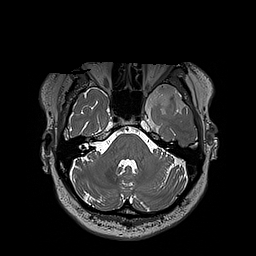
Brain MRI from a brain-tumour surgery series, one axial slice. Slice 147 of 192 in the series (ordered by position). 1 mm slice thickness. 256 × 256 image matrix, field of view 250 × 250 mm. From the clinical record (not read from this slice): histopathology: Oligodendroglioma; WHO grade: 3; IDH mutation: yes.
Annotated regions visible in this slice (manually delineated by an expert):
- tumour: bounding box <124,84,197,111> (left, top, right, bottom; pixels)